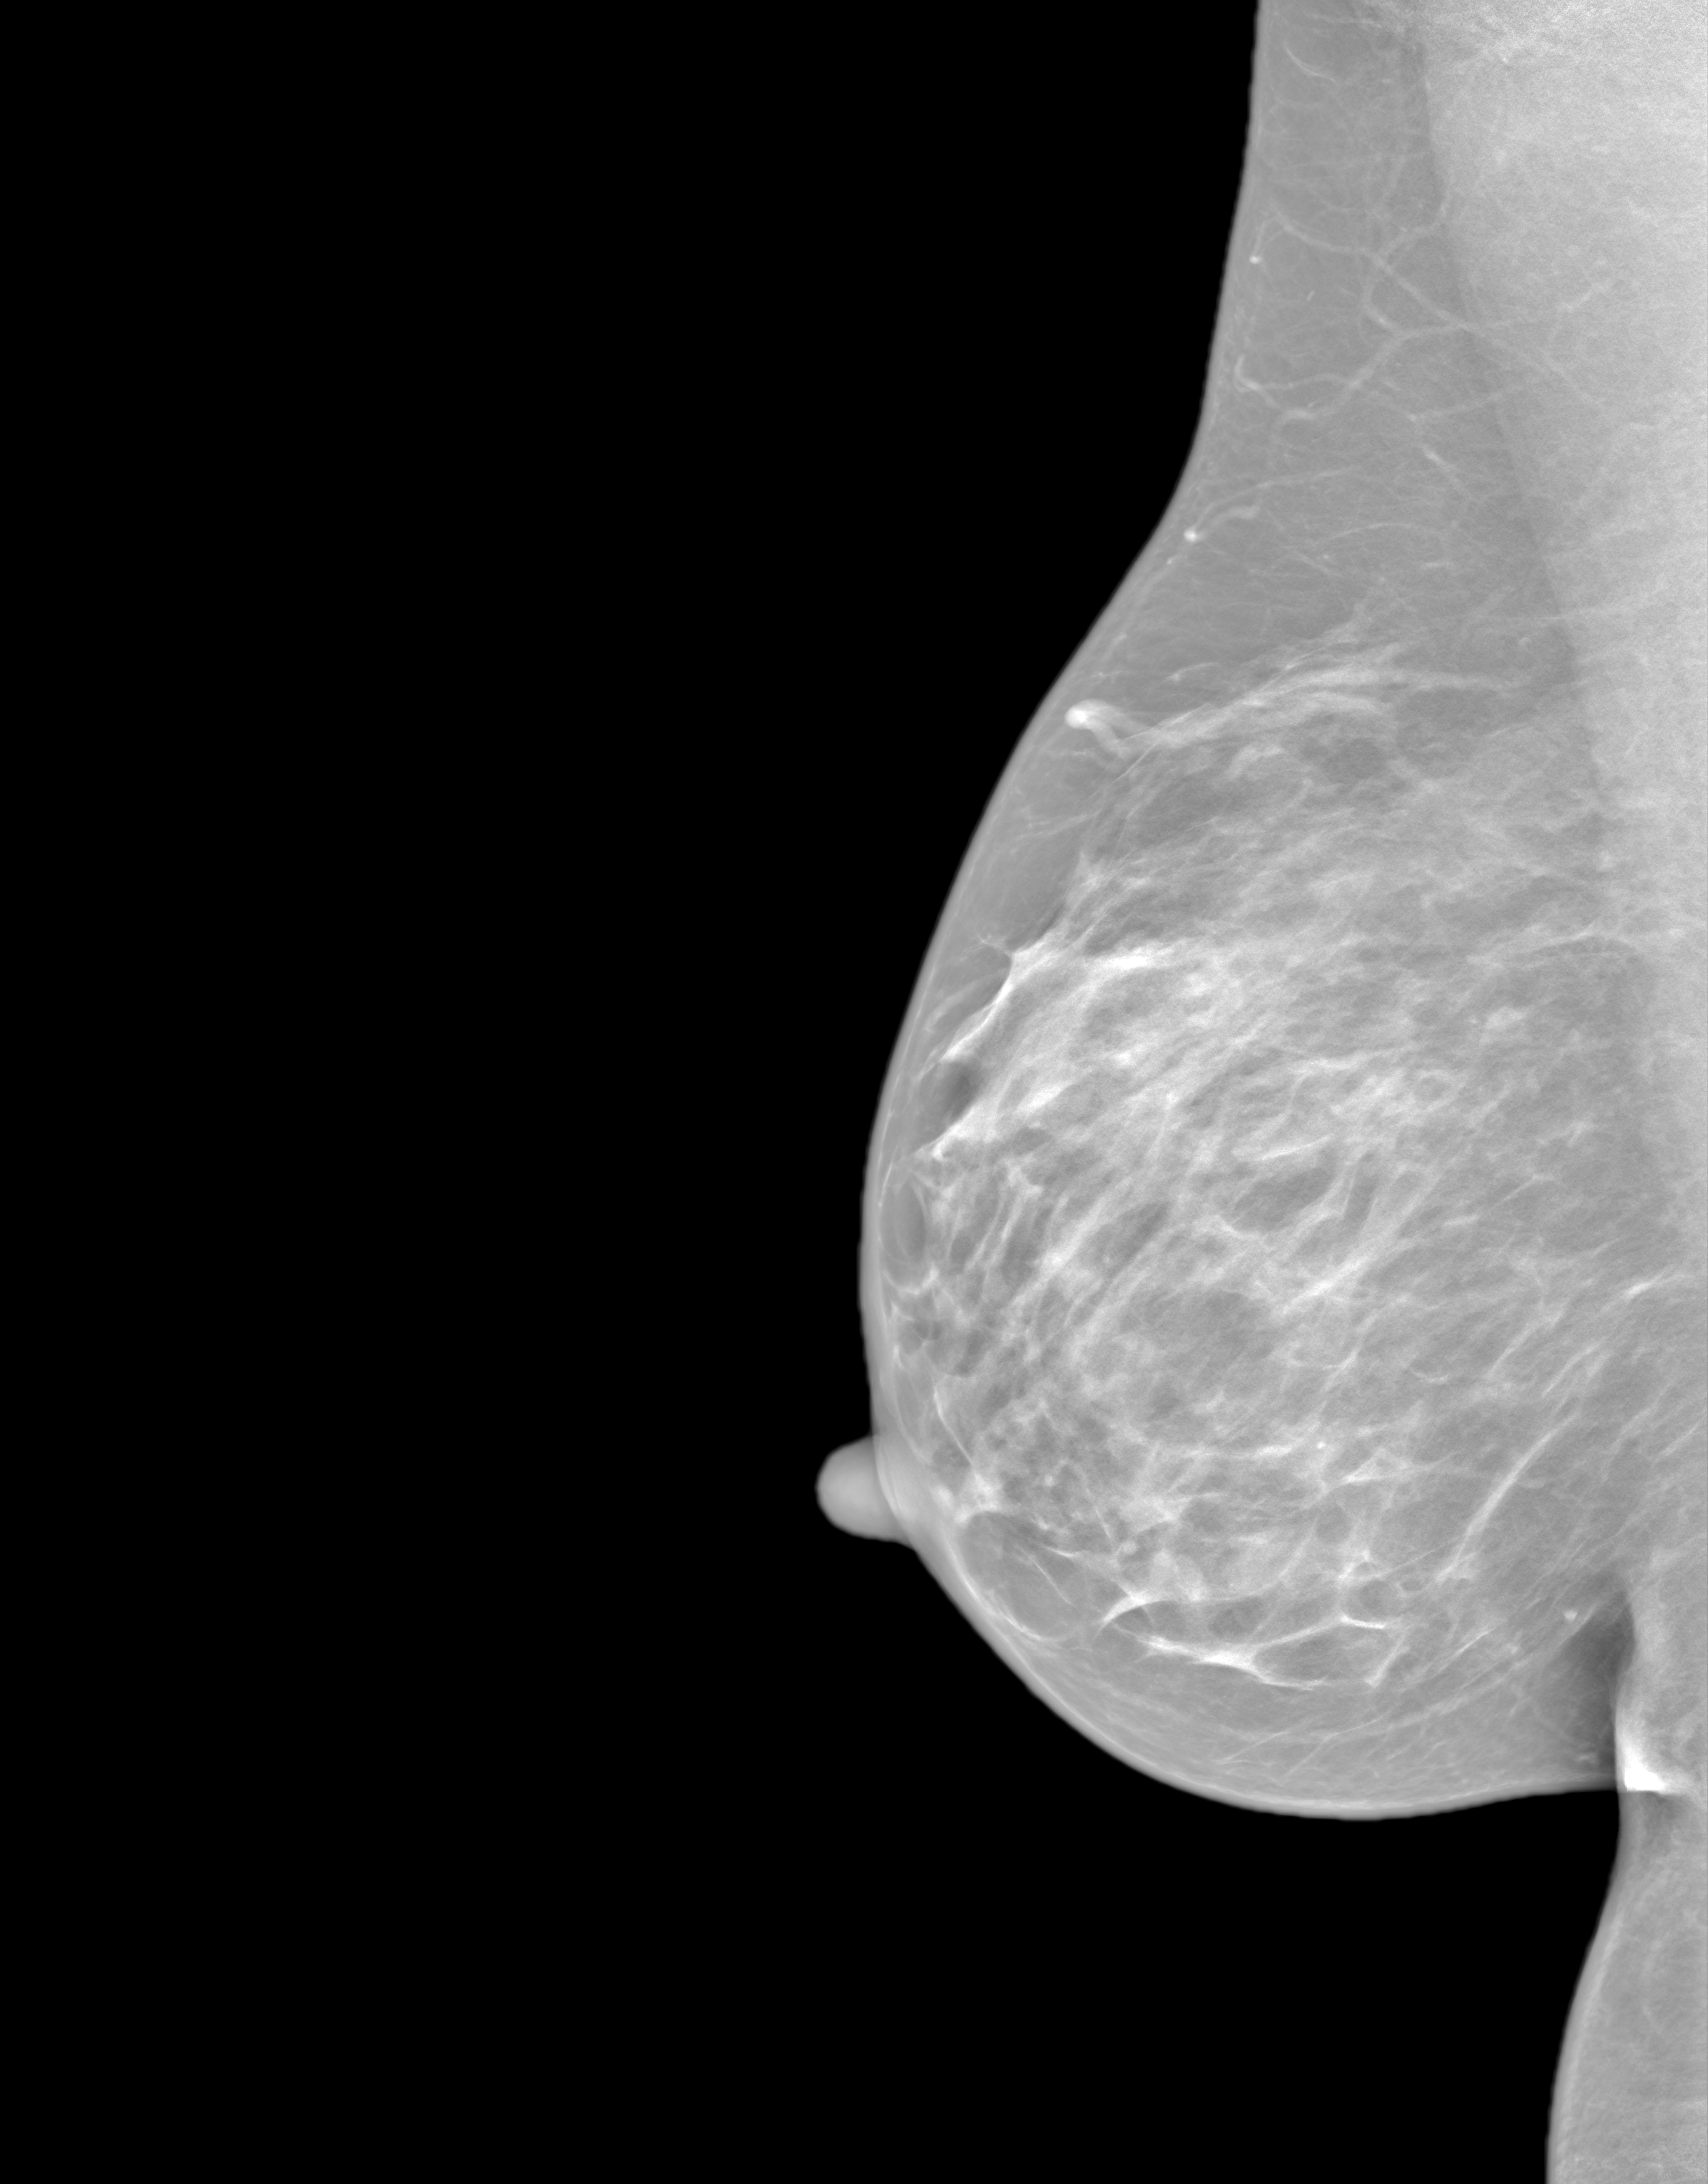
Synthesized 2-D mammogram reconstructed from digital breast tomosynthesis, right breast, medio-lateral oblique projection, screening examination. Patient: female, 49 years.
BI-RADS breast density category at the screening exam (both breasts, scale 1–4): 3. Final BI-RADS category for the screening round (tomosynthesis exam, both breasts): category 1. Recall: no recall after this screen.